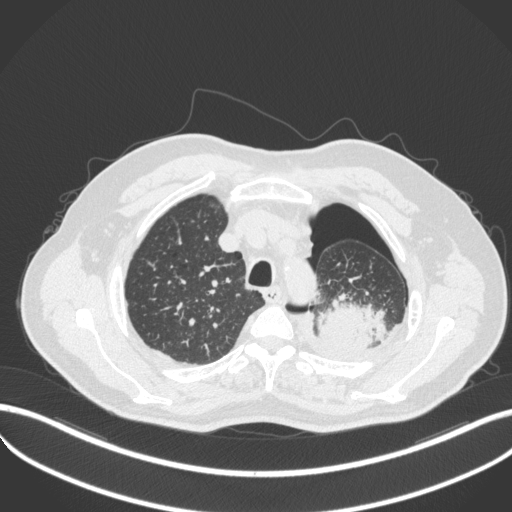
Chest CT, one axial slice; position 406 of 466 along the scan axis; reconstruction kernel B31f; lung window (W 1500 / L -600 HU); 512 × 512 image matrix, field of view 400 × 400 mm. Male patient, age 76 years. From the clinical record (not read from this slice): clinical TNM (as recorded): T3 N0 M1b.
Outlined on this slice (bounding box drawn by a radiologist):
- lung tumour (recorded histology: adenocarcinoma): bounding box [x1, y1, x2, y2] px = [313, 298, 388, 353]